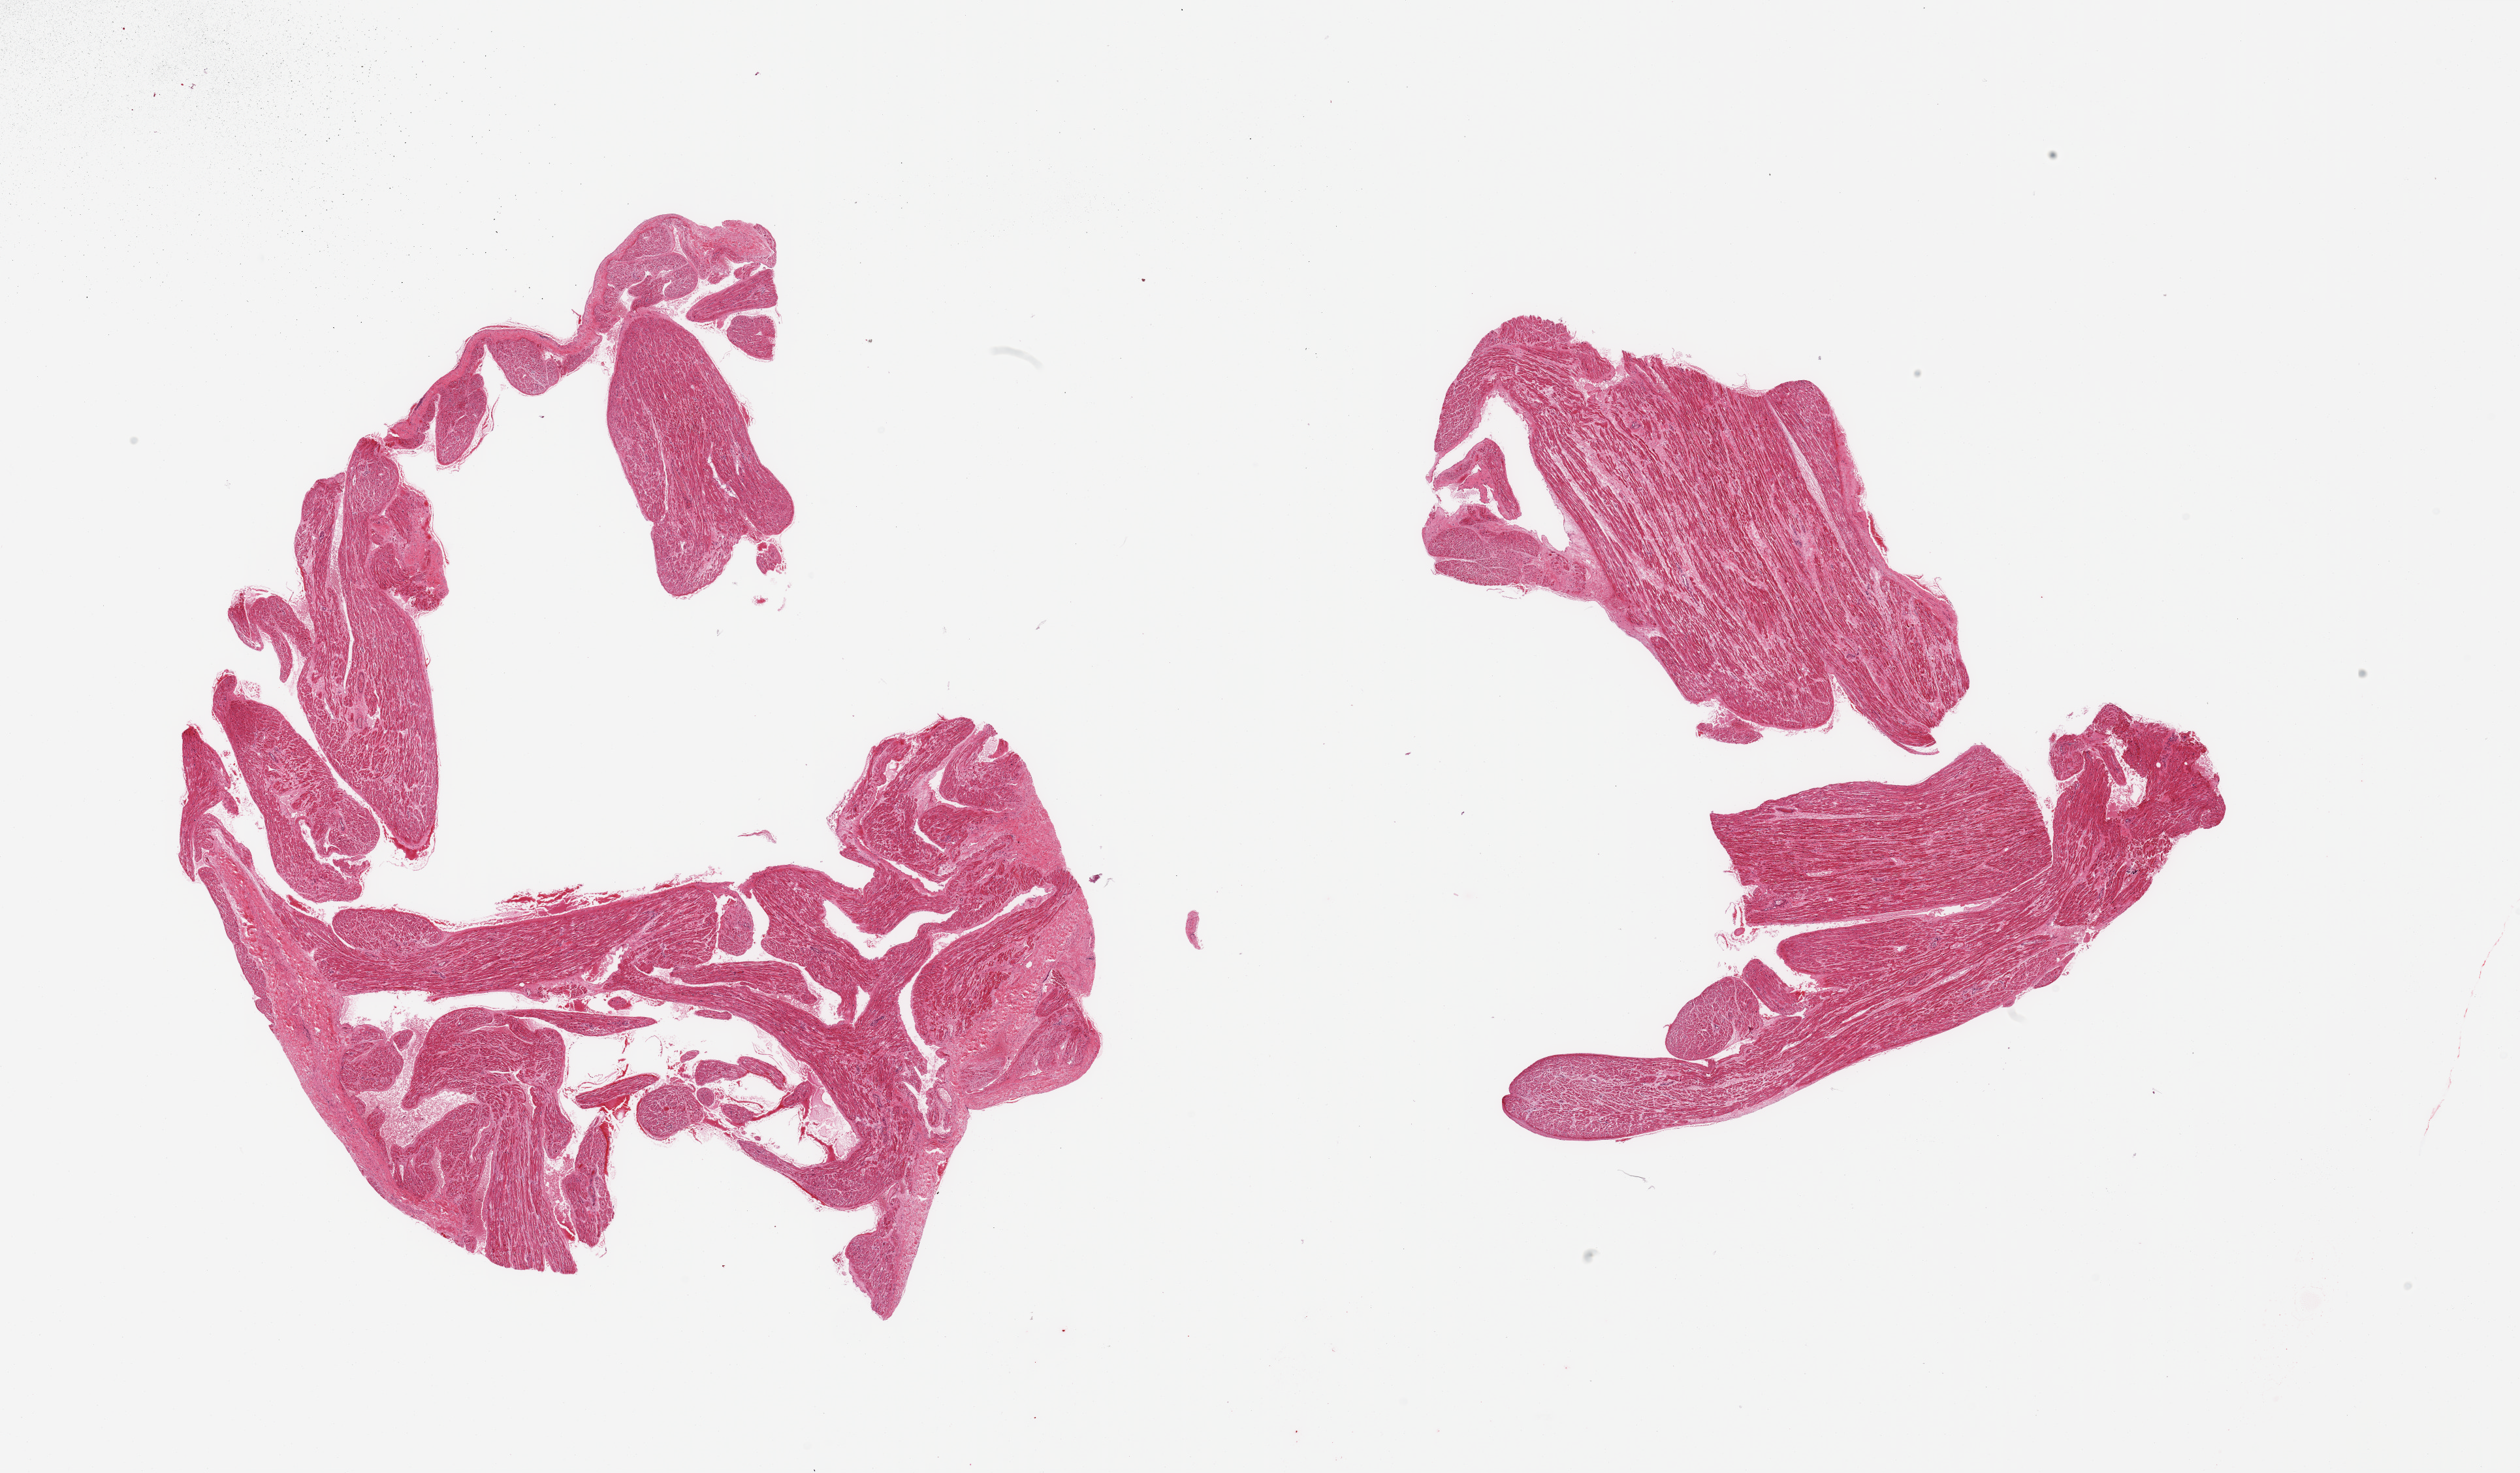
Digitized H&E-stained section — shown as a low-resolution overview of the whole scanned area (about 30.5 x 17.8 mm, from a 20x scan); PAXgene-fixed, paraffin-embedded tissue; sampled site (target tissue): auricular appendage; tissue donor sample. Donor sex: male.
* review note (as recorded): 2 pieces; minimal stromal content